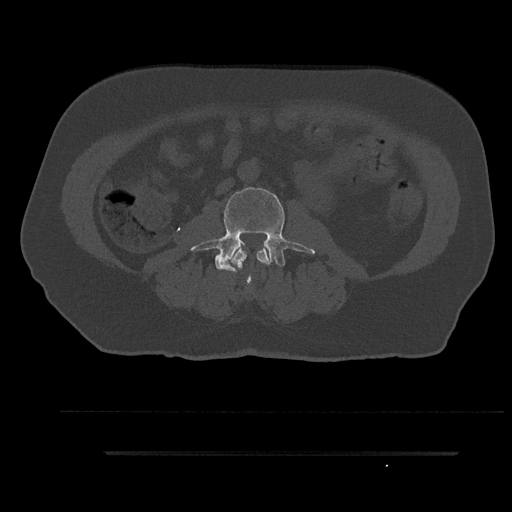
CT including the spine, one axial slice; slice 59 of 797 in the series (ordered by position); bone window (W 1800 / L 400 HU); 512 × 512 image matrix, field of view 432 × 432 mm. Male patient, age 63 years. Case-level facts recorded for this patient, not image findings: primary cancer: renal.
Outlined on this slice (semi-automatic segmentation, software-assisted and operator-edited):
- L2 vertebra: bounding box (x1, y1, x2, y2) in pixels: (232, 248, 270, 272)
- L3 vertebra: (190, 185, 315, 281)